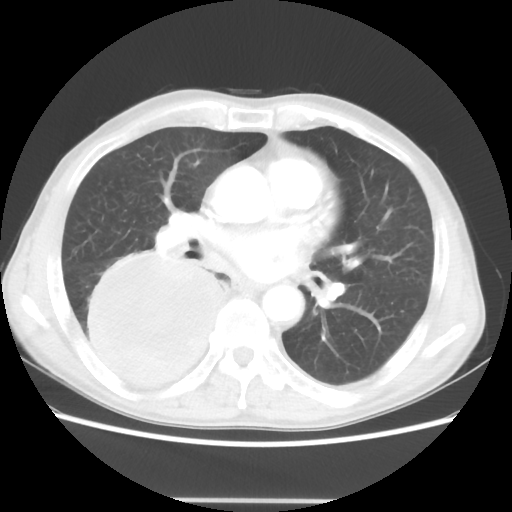
Chest CT, one axial slice; lung window (W 1500 / L -600 HU); 512 × 512 image matrix, field of view 361 × 361 mm. Patient: male, 66 years. Case-level facts recorded for this patient, not image findings: clinical TNM (as recorded): T4 N1 M1.
Annotated regions visible in this slice (rectangle marked by the reading radiologist):
- lung tumour (recorded histology: small cell carcinoma): box from (x=78, y=240) to (x=224, y=401) px